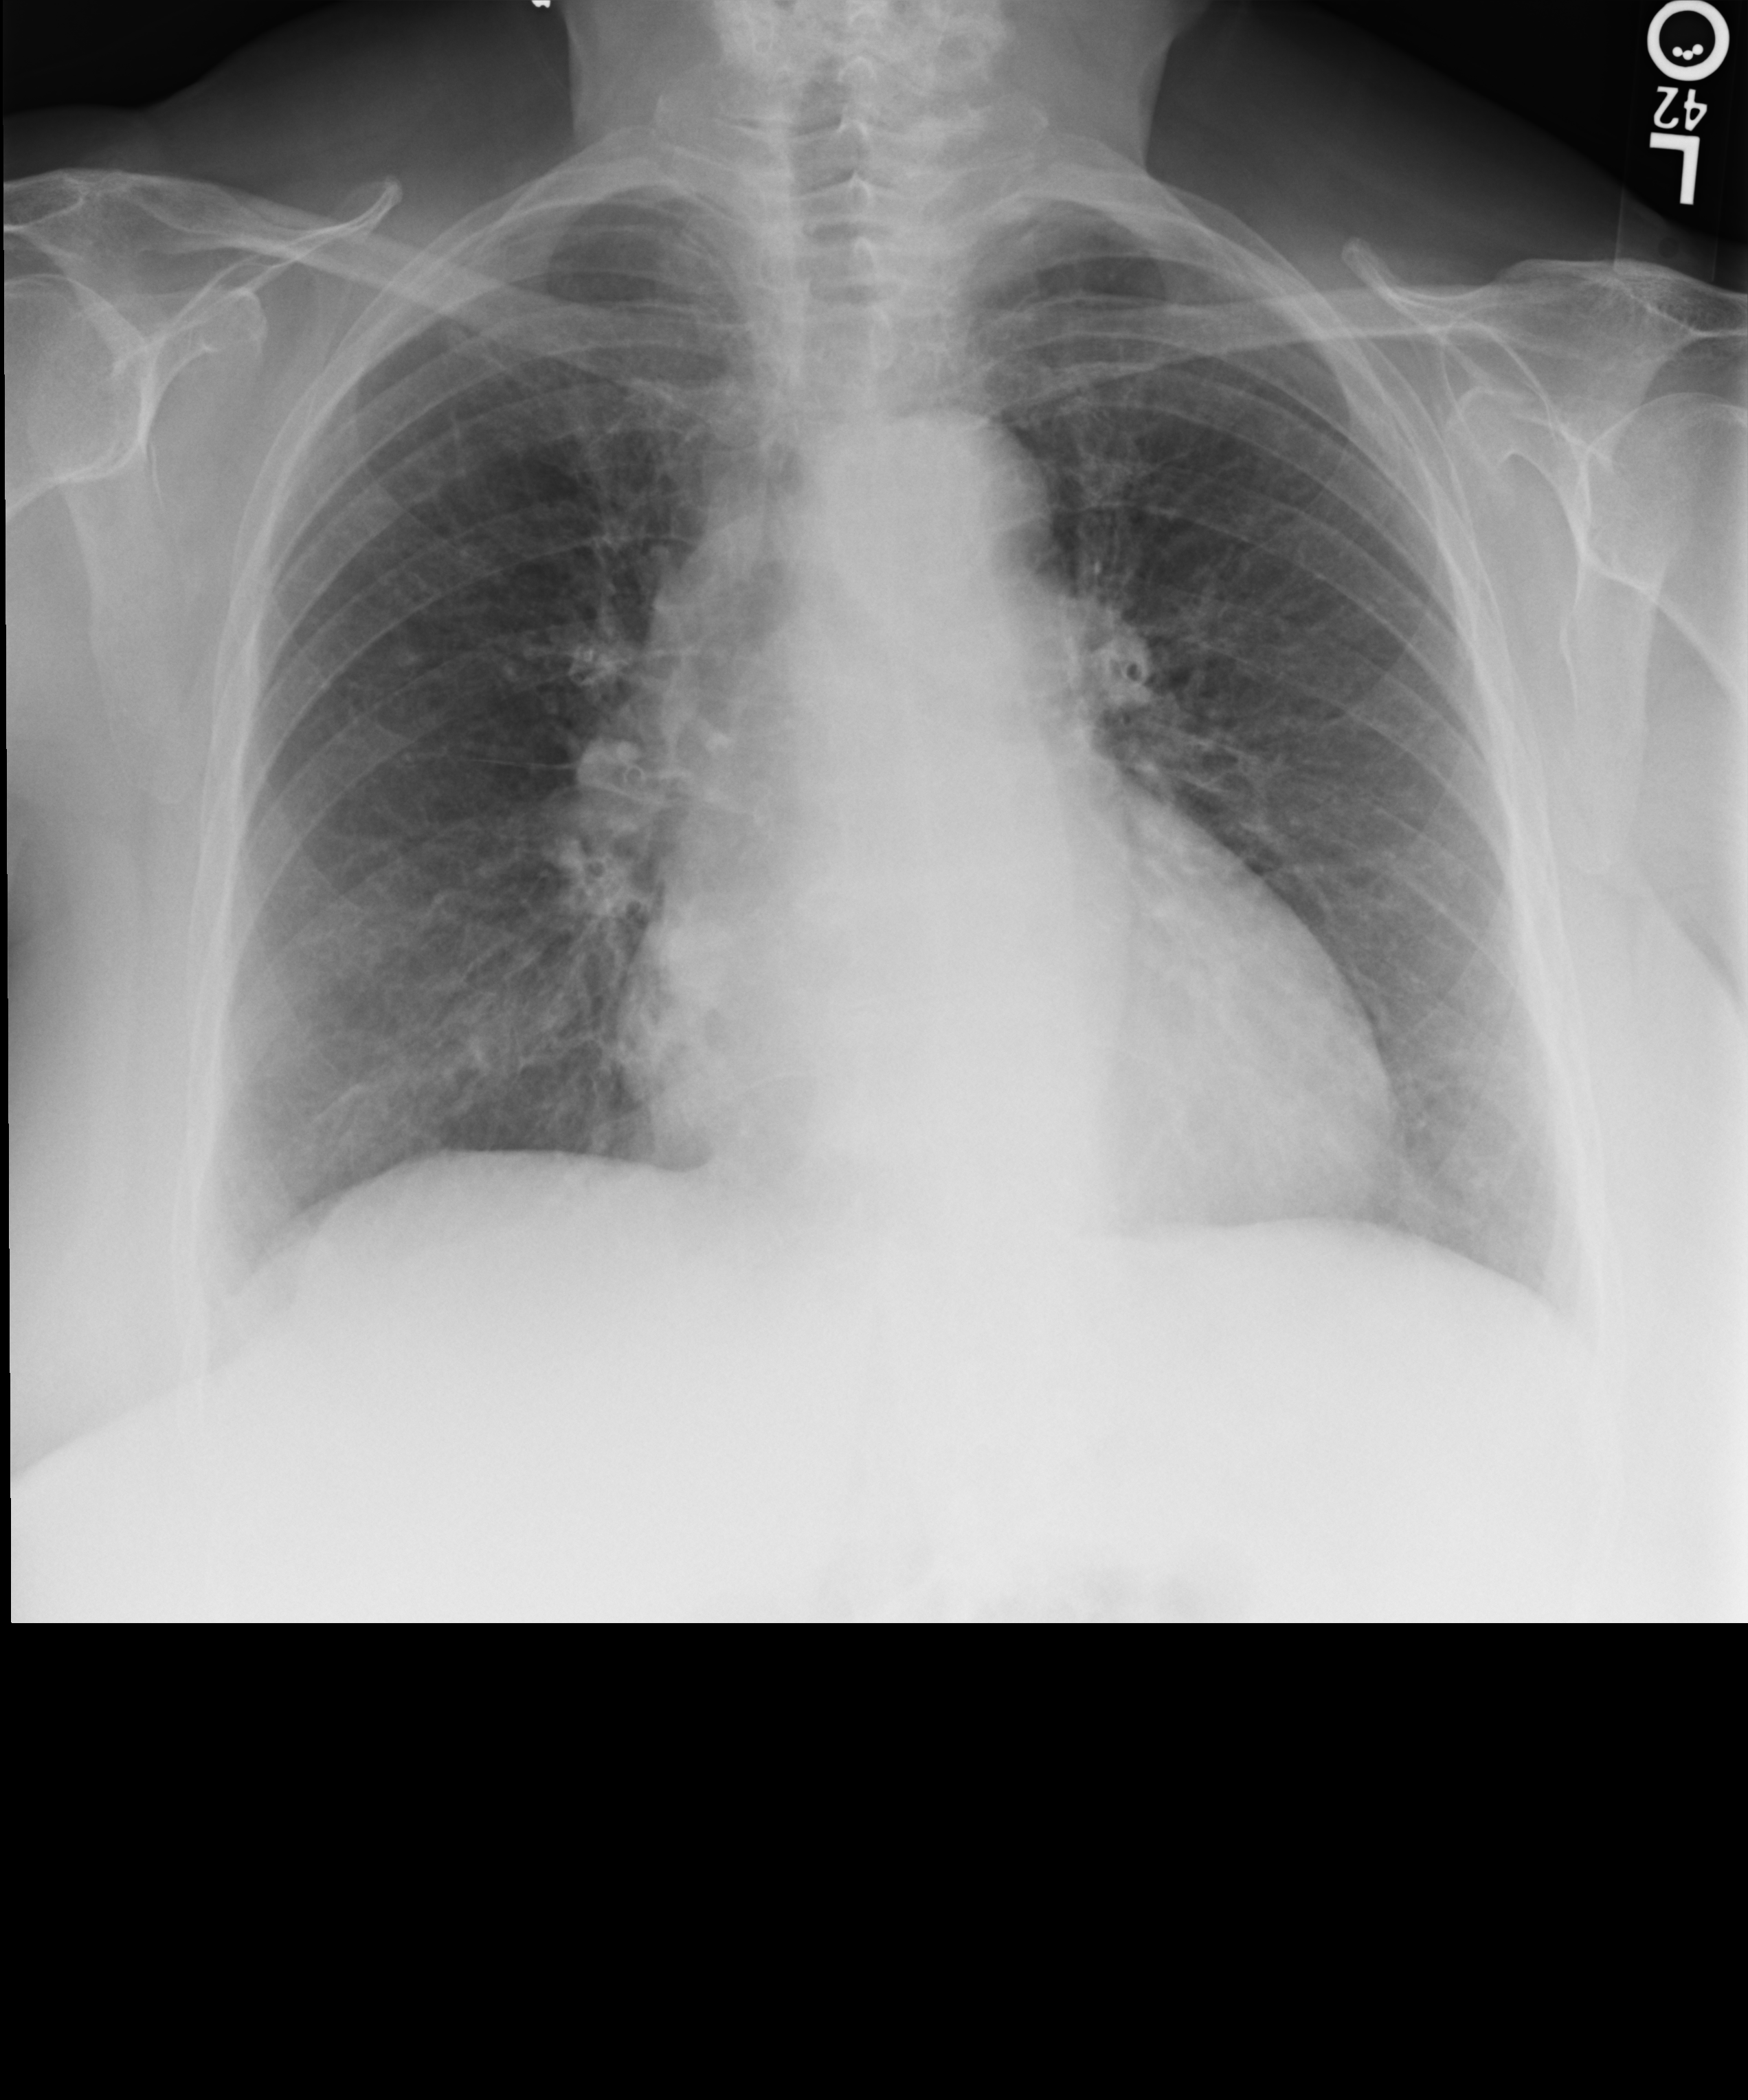
Chest radiograph; posteroanterior (PA) projection. Patient hospitalised with COVID-19; female, aged 75–90 years.
Hospital-stay facts (about this admission, not read from this image; timing relative to this image not recorded):
- length of hospital stay: 5 days
- mechanically ventilated during this hospital stay: no